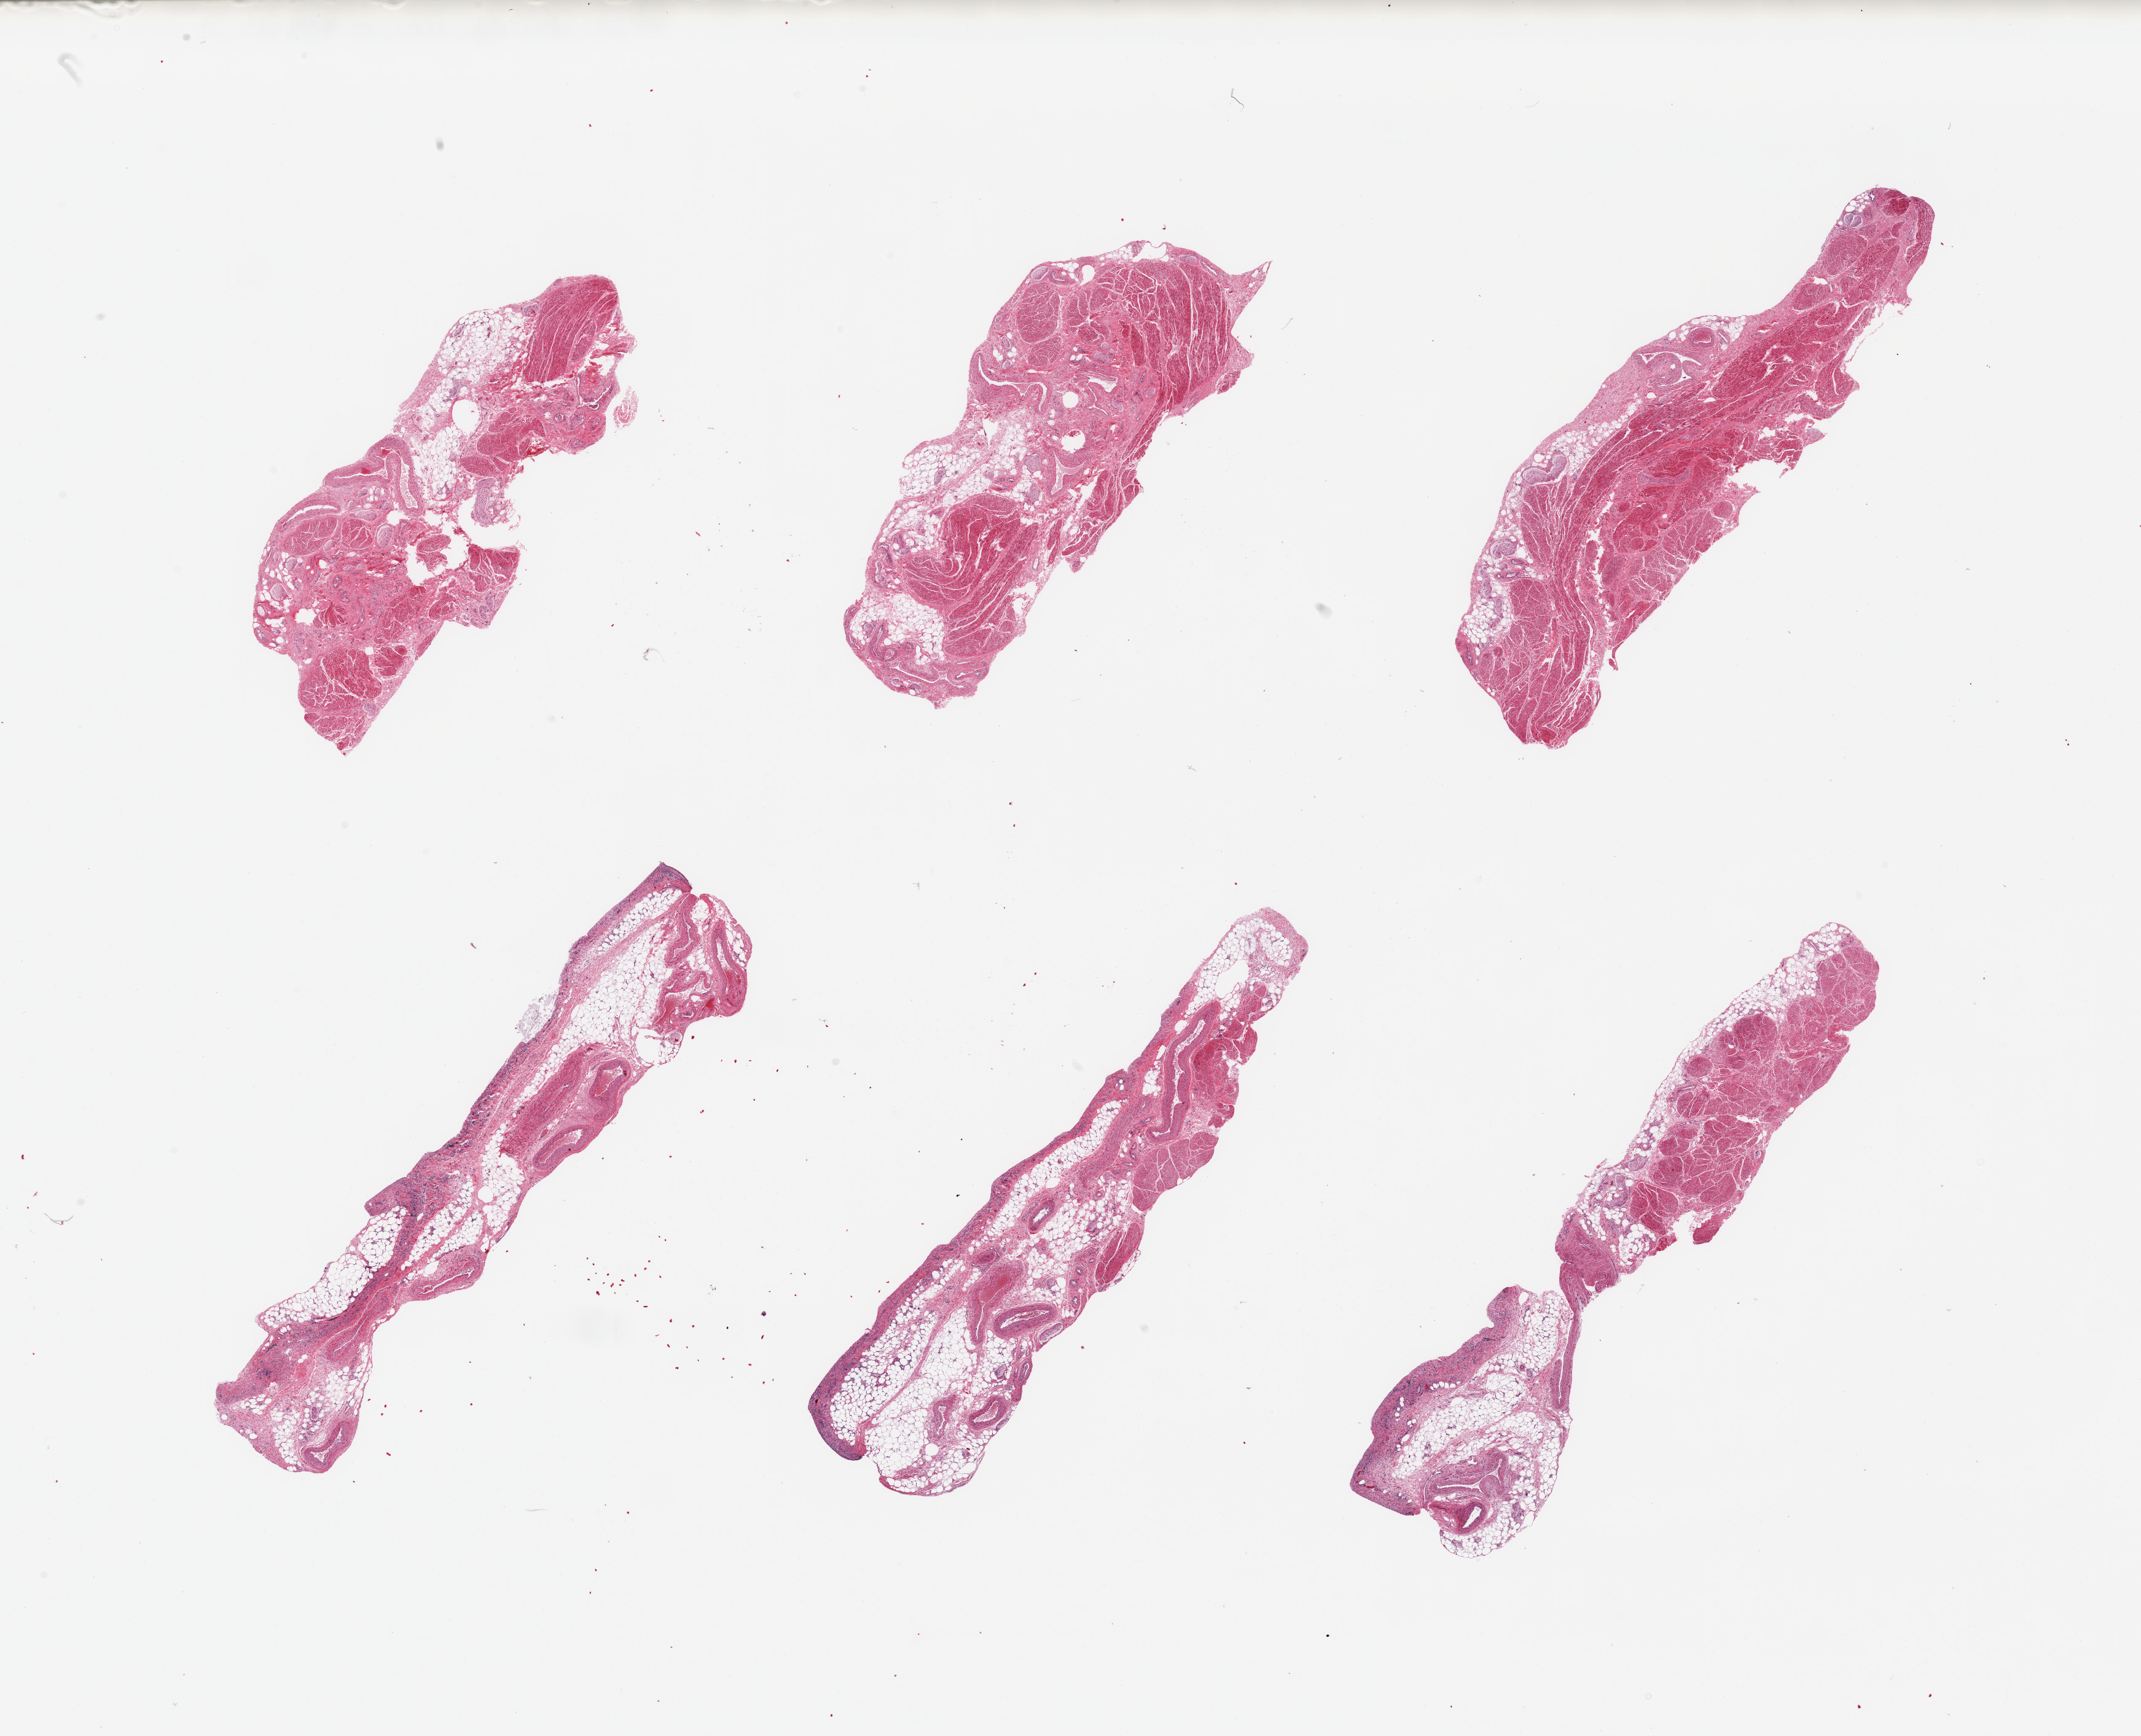
Hematoxylin and eosin (H&E) whole-slide image — a low-resolution overview of the entire scanned area, about 27.6 x 22.4 mm (from a 20x scan). PAXgene-fixed paraffin-embedded (PFPE) section. Target tissue: vagina. Tissue donor sample. Donor: female.
Pathologist's review note for this sample: 6 pieces; fibromuscular tissue without a mucosa; not vagina, possibly bladder.